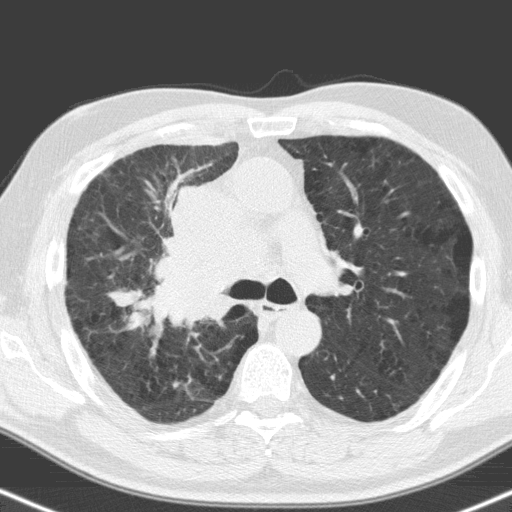
Low-dose screening chest CT, one axial slice; slice 107 of 160 in the series (ordered by position); 120 kVp; lung window (W 1500 / L -600 HU); 3.2 mm slice thickness; 512 × 512 image matrix, field of view 324 × 324 mm.
Outlined on this slice (outlined manually by an expert reader):
- lesion 1 (tumor, hilum of right lung): bounding box (x1, y1, x2, y2) in pixels: (154, 185, 266, 320)
- lesion 2 (tumor, upper lobe of right lung): (115, 290, 137, 307)